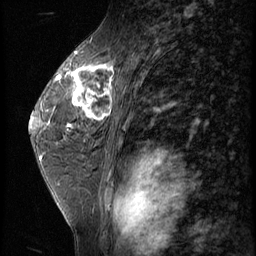
Breast MRI (dynamic contrast-enhanced), one sagittal slice. Position 37 of 62 along the scan axis. 3 images stored at this slice position (order not interpretable as contrast timing). 1.5 T. TE 4.2 ms, TR 9 ms. 256 × 256 image matrix, field of view 180 × 180 mm. Female patient, age 44 years. Case-level facts recorded for this patient, not image findings: setting: breast cancer imaged before/during neoadjuvant chemotherapy; receptor status: triple-negative.
Annotated regions visible in this slice (semi-automatically segmented with operator editing):
- analysis volume of interest (the breast-tissue region the enhancement analysis was run in; not a lesion): box from (x=67, y=64) to (x=116, y=125) px
- tumour enhancement mask (voxels above the 140 % enhancement threshold inside the analysis volume of interest): (x=68, y=64)–(x=115, y=122)